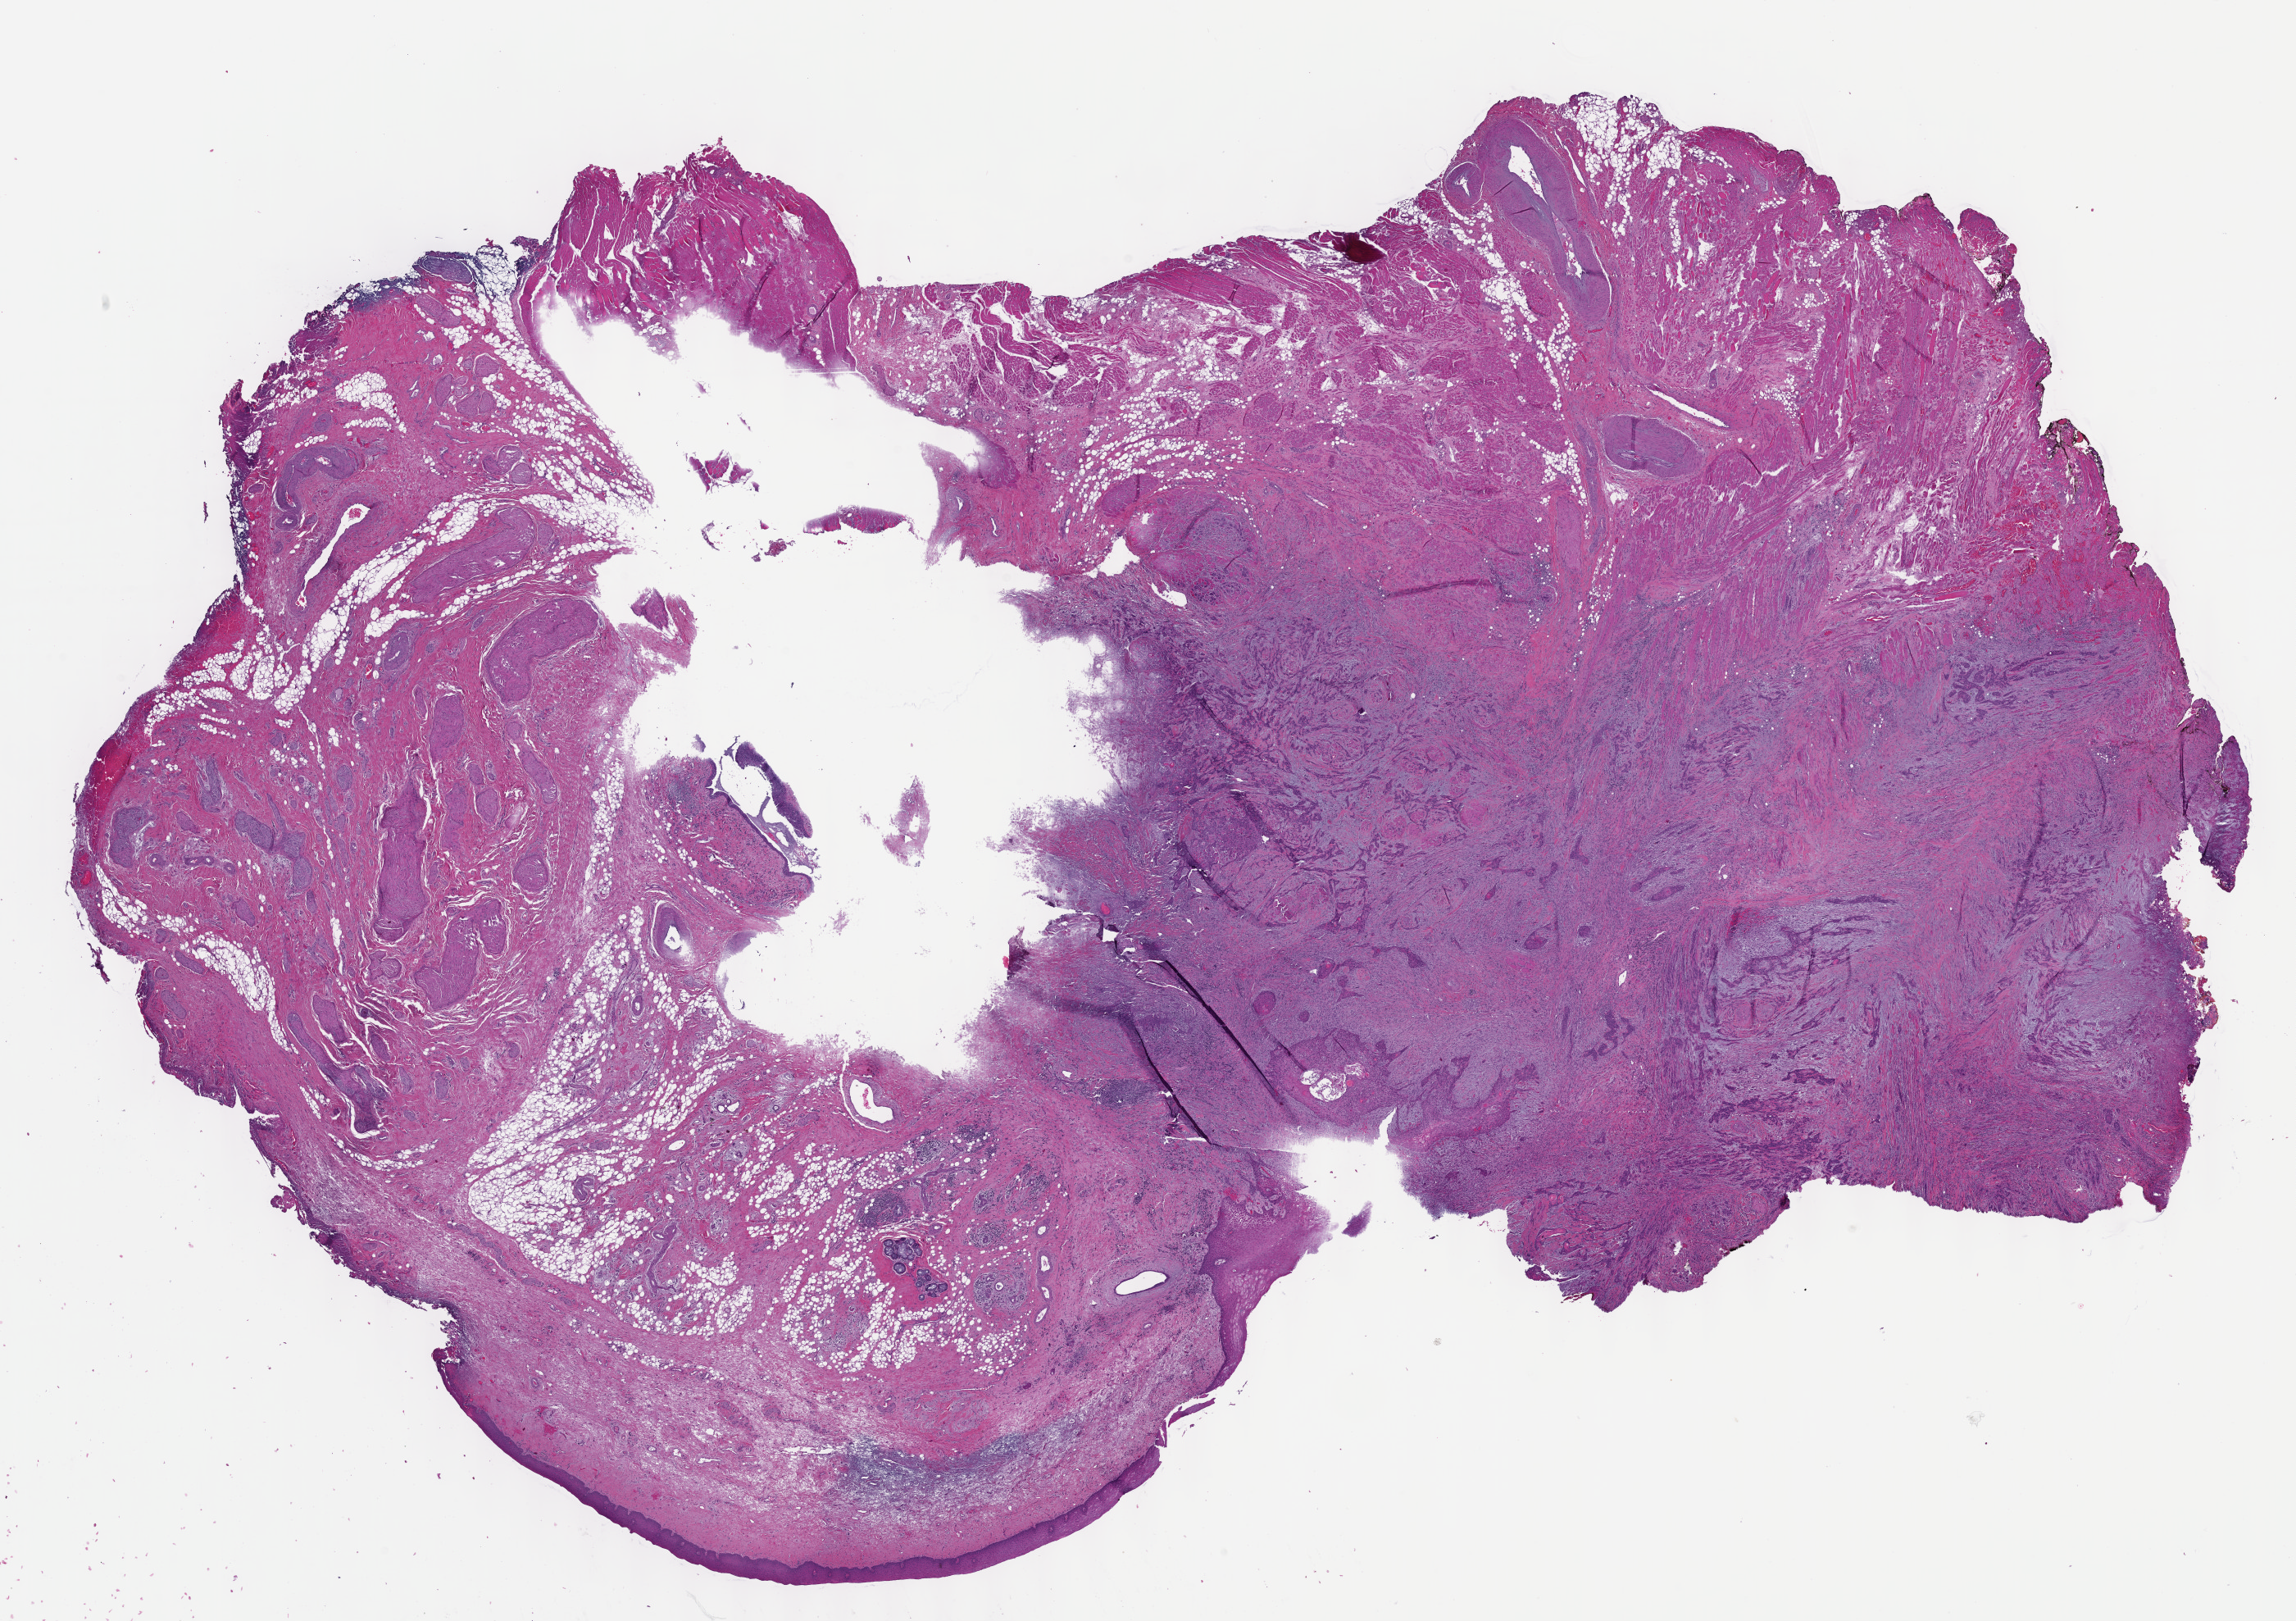
Whole-slide histology image, Hematoxylin and eosin (H&E) stained, a low-resolution overview of the entire scanned area, about 22.6 x 16.0 mm; formalin-fixed paraffin-embedded (FFPE) diagnostic section; sample: primary tumour, head and neck. Female, age 87 years at initial diagnosis. Histologic grade: G3 (poorly differentiated).
* AJCC pathologic stage: I
* pathologic diagnosis: Squamous cell carcinoma, NOS (tongue, NOS)
* TNM: T1 NX